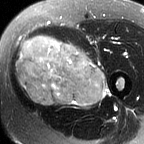
MRI of an extremity soft-tissue mass, one axial slice; slice 28 of 60 in the series (ordered by position); T2-weighted fat-saturated; MR volume resampled by the dataset authors to the PET/CT grid (not the native acquisition matrix); 3.27 mm slice thickness; 144 × 144 image matrix. Female patient. From the clinical record (not read from this slice): histological type: pleiomorphic leiomyosarcoma; grade: intermediate; site of the primary tumour: left thigh.
Annotated regions visible in this slice (expert contour drawn on MRI and transferred to this co-registered scan by the dataset authors):
- gross tumour volume including surrounding oedema: bounding box [x1, y1, x2, y2] px = [15, 37, 110, 109]
- gross tumour volume (mass): [15, 37, 105, 105]